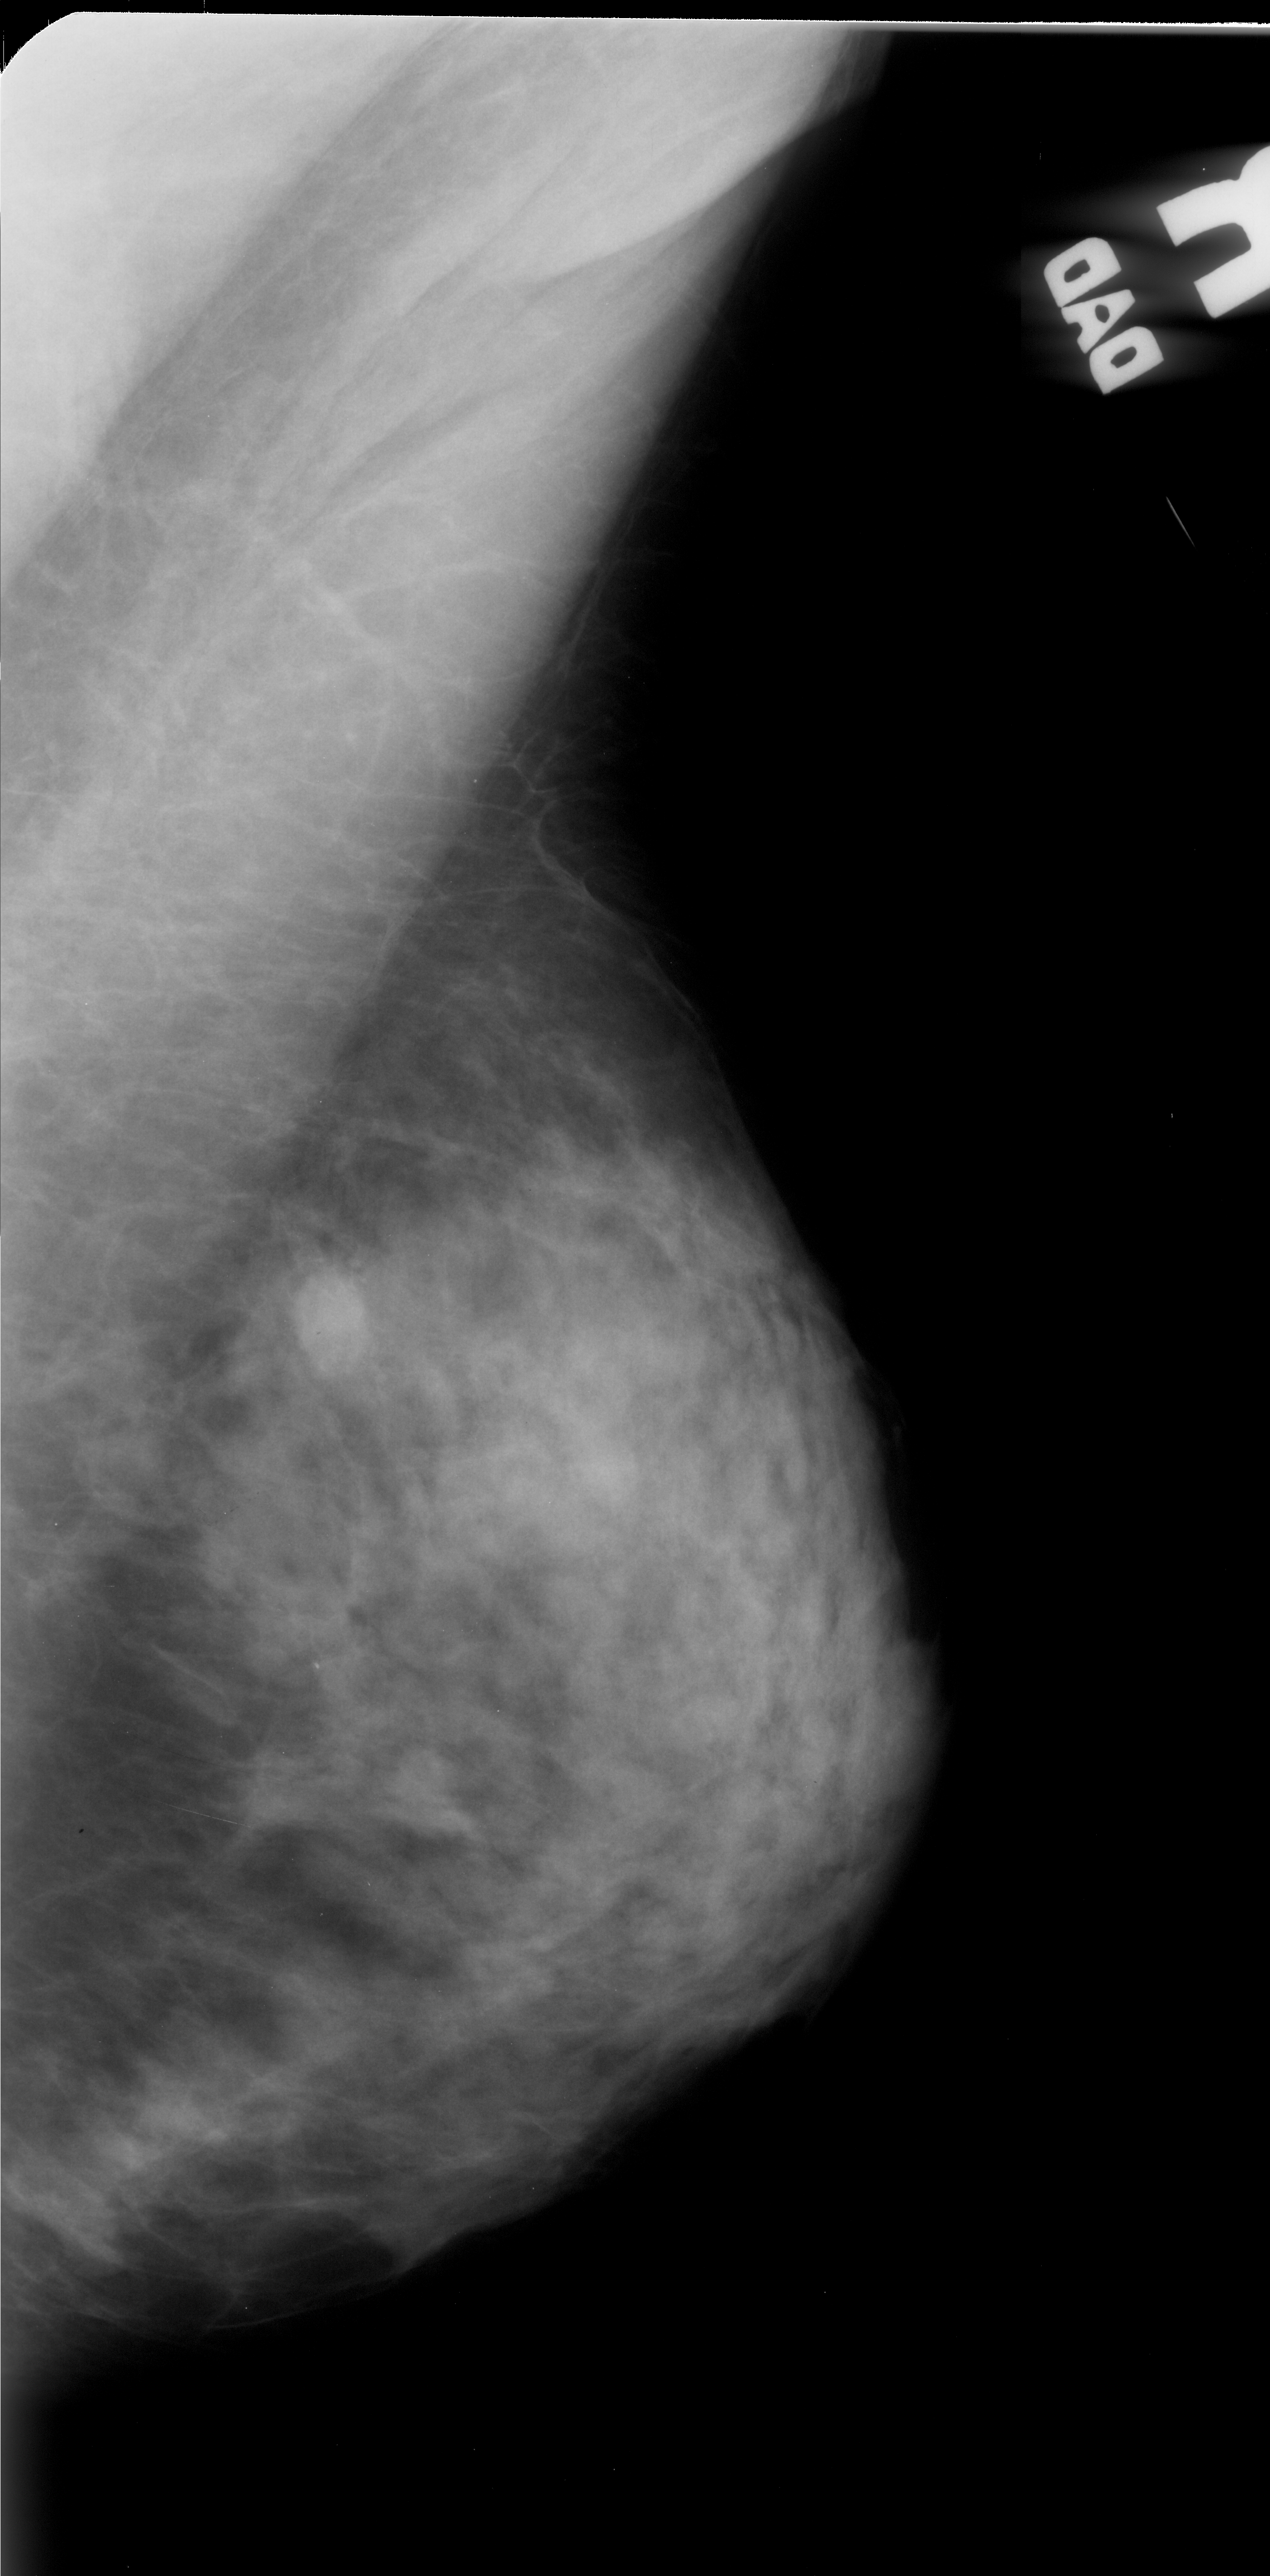
Scanned film-screen mammogram; right breast; mediolateral oblique (MLO) view; breast composition: heterogeneously dense (BI-RADS density category 3 of 4); 1270 × 2576 image matrix.
Marked abnormalities (boxes around the expert regions of interest):
- mass, shape oval, margins ill defined; BI-RADS assessment category 4; pathology (as recorded): malignant: box from (x=285, y=1251) to (x=374, y=1365) px